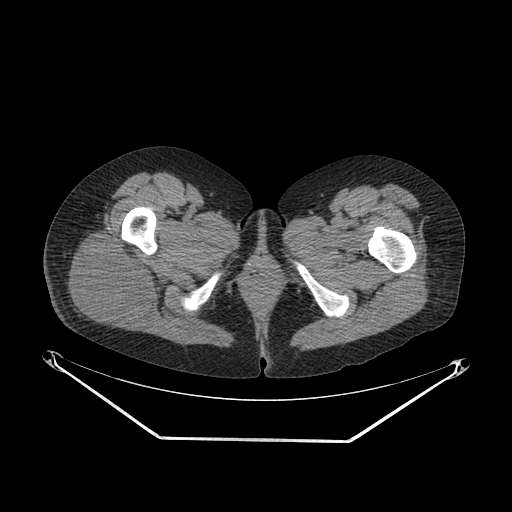
CT of an extremity soft-tissue mass (from a PET/CT study), one axial slice. Position 33 of 267 along the scan axis. Soft-tissue window (W 400 / L 40 HU). 3.75 mm slice thickness. 512 × 512 image matrix. Female patient. From the clinical record (not read from this slice): histological type: epithelioid sarcoma with vascular differentiation; site of the primary tumour: right buttock.
Outlined on this slice (expert contour drawn on MRI and transferred to this co-registered scan by the dataset authors):
- gross tumour volume (mass): box from (x=66, y=235) to (x=152, y=323) px